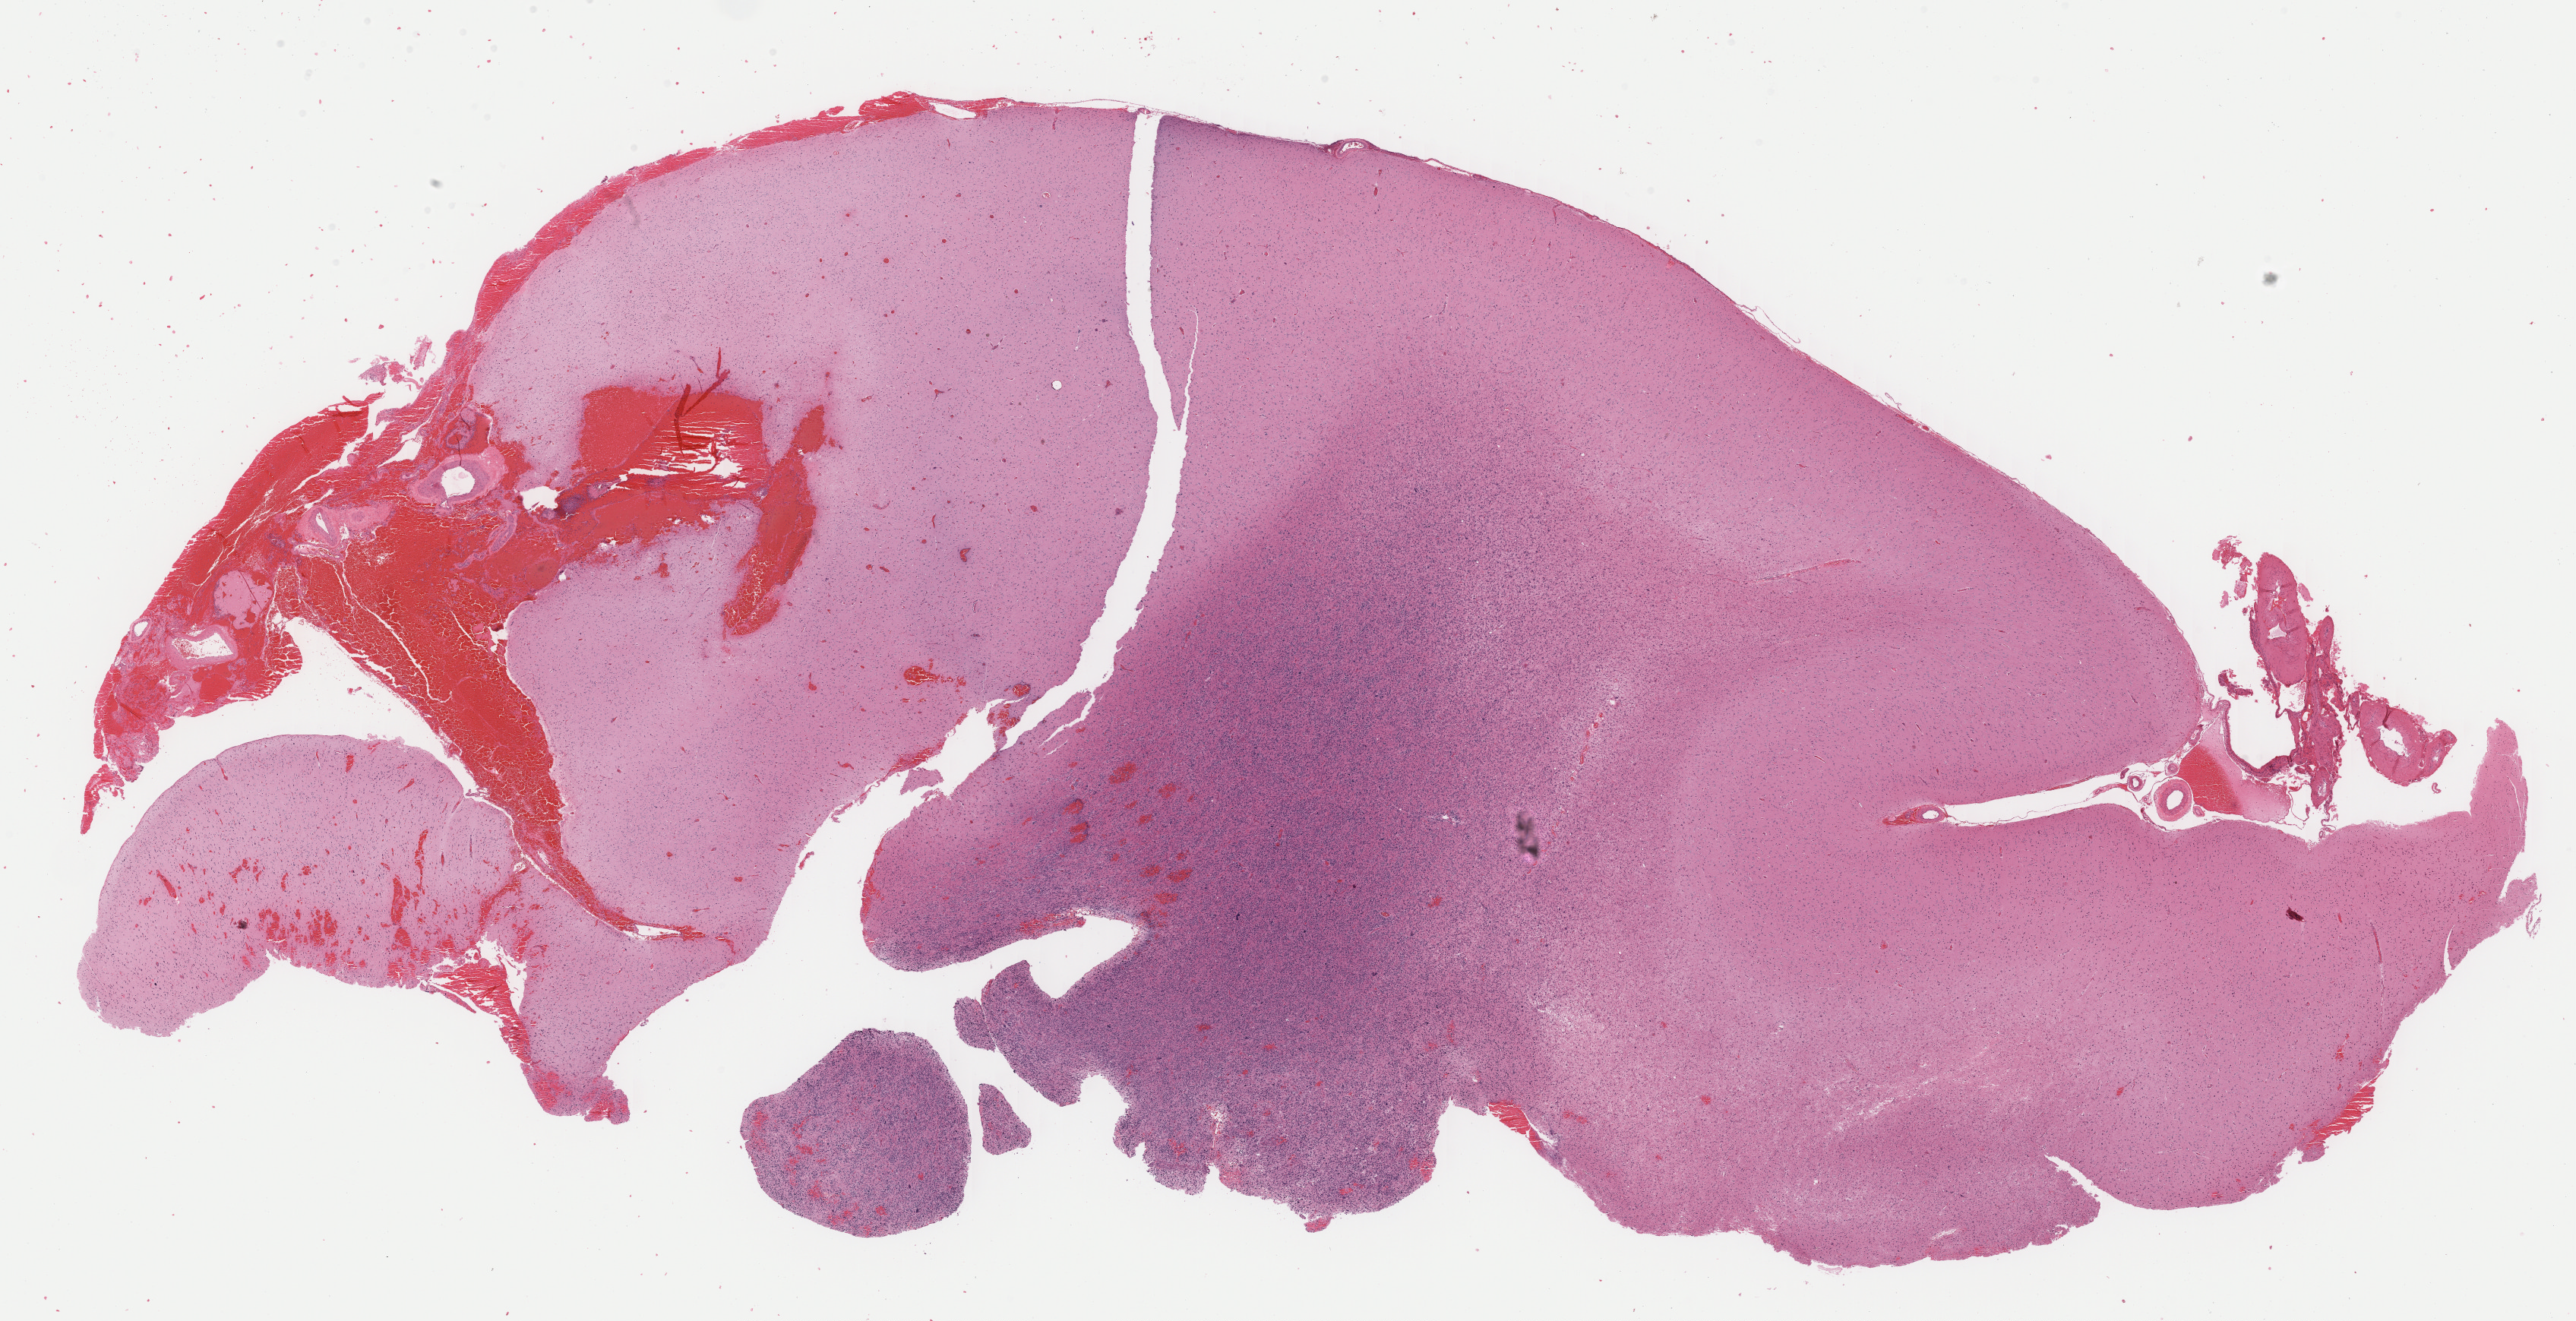
Digitized H&E-stained tissue section (whole slide), a low-resolution overview of the entire scanned area, about 26.7 x 13.7 mm. FFPE section. Brain, primary tumour sample. Male patient; age at initial diagnosis 65 years.
Diagnosis: Glioblastoma.